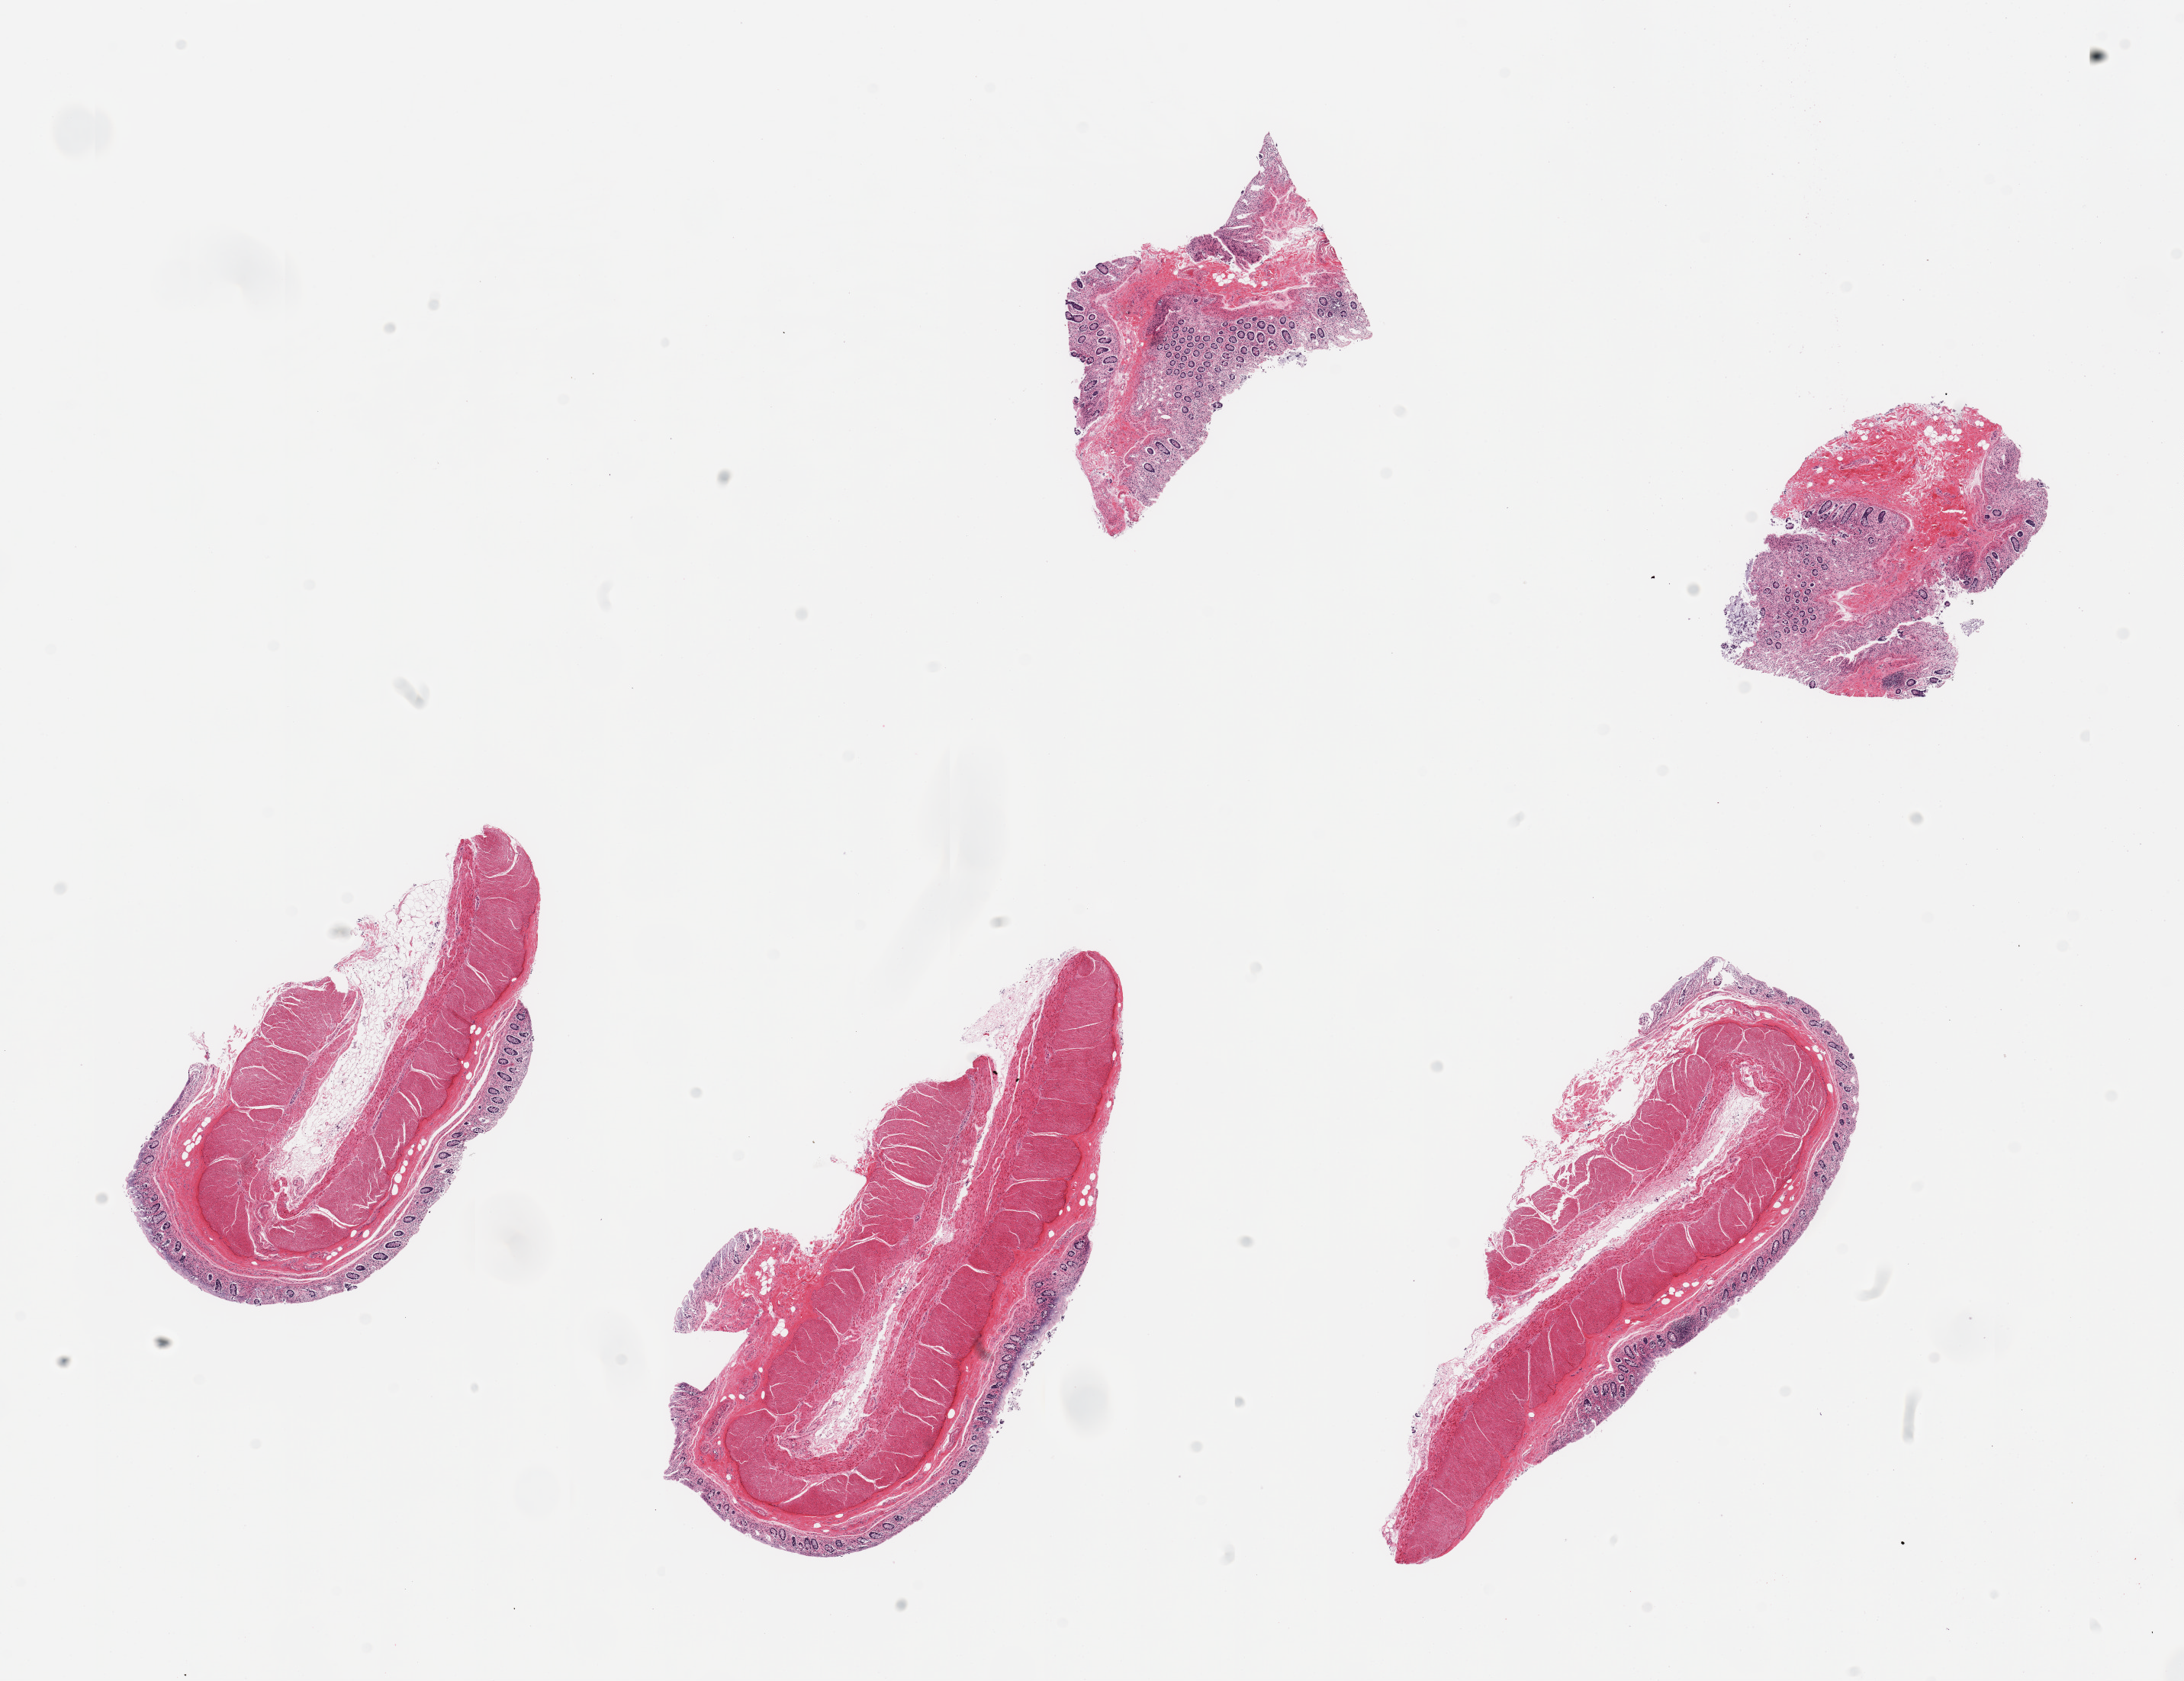
Digitized H&E-stained section, low-resolution overview of the scanned area, about 22.6 x 17.4 mm (slide scanned at 20x), PAXgene-fixed, paraffin-embedded tissue, section of transverse colon (target tissue), donor tissue sample. Donor sex: male.
• review note (as recorded): 6 pieces, mucosa up to ~0.2mm thick, badly autolyzed/sloughed